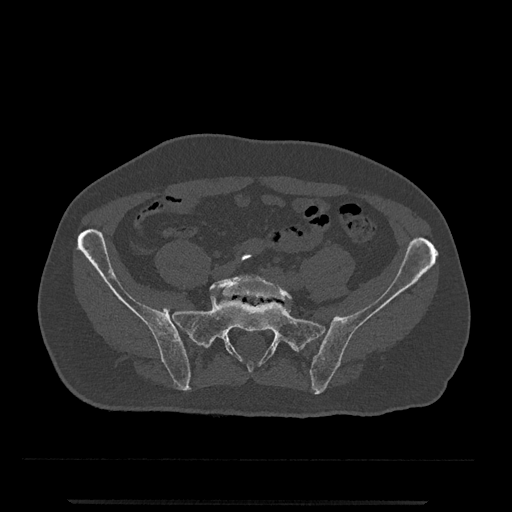
CT including the spine, one axial slice; position 26 of 797 along the scan axis; 120 kVp; bone window (W 1800 / L 400 HU); 0.5 mm slice thickness; 512 × 512 image matrix. Male patient, age 63 years. From the clinical record (not read from this slice): primary cancer: prostate.
Outlined on this slice (semi-automatically segmented with operator editing):
- L5 vertebra: bounding box (x1, y1, x2, y2) in pixels: (210, 275, 292, 302)